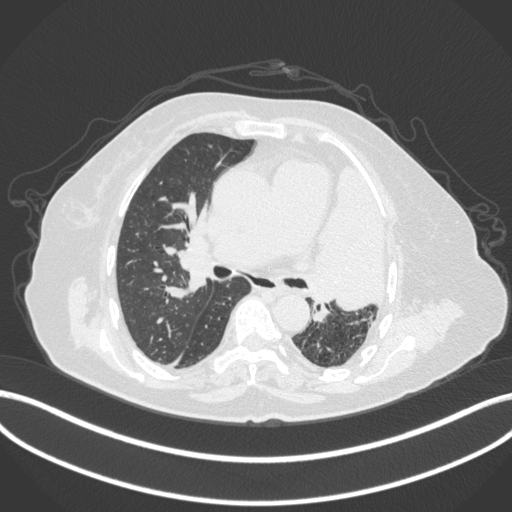
Chest CT, one axial slice; slice 224 of 399 in the series (ordered by position); reconstruction kernel B31f; 120 kVp; lung window (W 1500 / L -600 HU); 1 mm slice thickness; 512 × 512 image matrix. Female patient, age 75 years. From the clinical record (not read from this slice): clinical TNM (as recorded): T3 N3 M1.
Annotated regions visible in this slice (rectangle marked by the reading radiologist):
- lung tumour (recorded histology: adenocarcinoma): bounding box (x1, y1, x2, y2) in pixels: (311, 159, 387, 318)